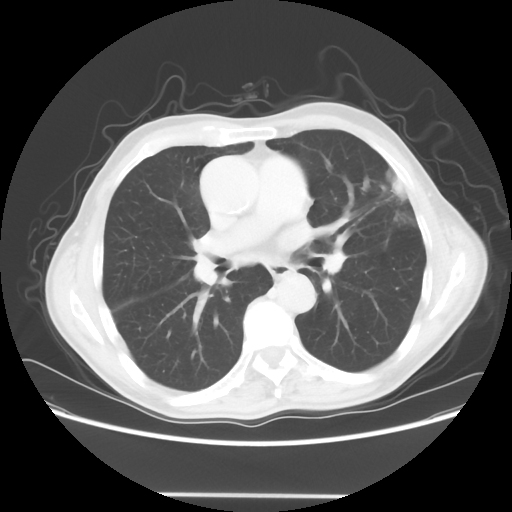
Chest CT, one axial slice. Position 35 of 64 along the scan axis. 120 kVp. Lung window (W 1500 / L -600 HU). 5 mm slice thickness. 512 × 512 image matrix. Male patient, age 71 years. Case-level facts recorded for this patient, not image findings: clinical TNM (as recorded): T1c N0 M0.
Structures marked on this image (rectangle marked by the reading radiologist):
- lung tumour (recorded histology: adenocarcinoma): bounding box <375,161,419,211> (left, top, right, bottom; pixels)